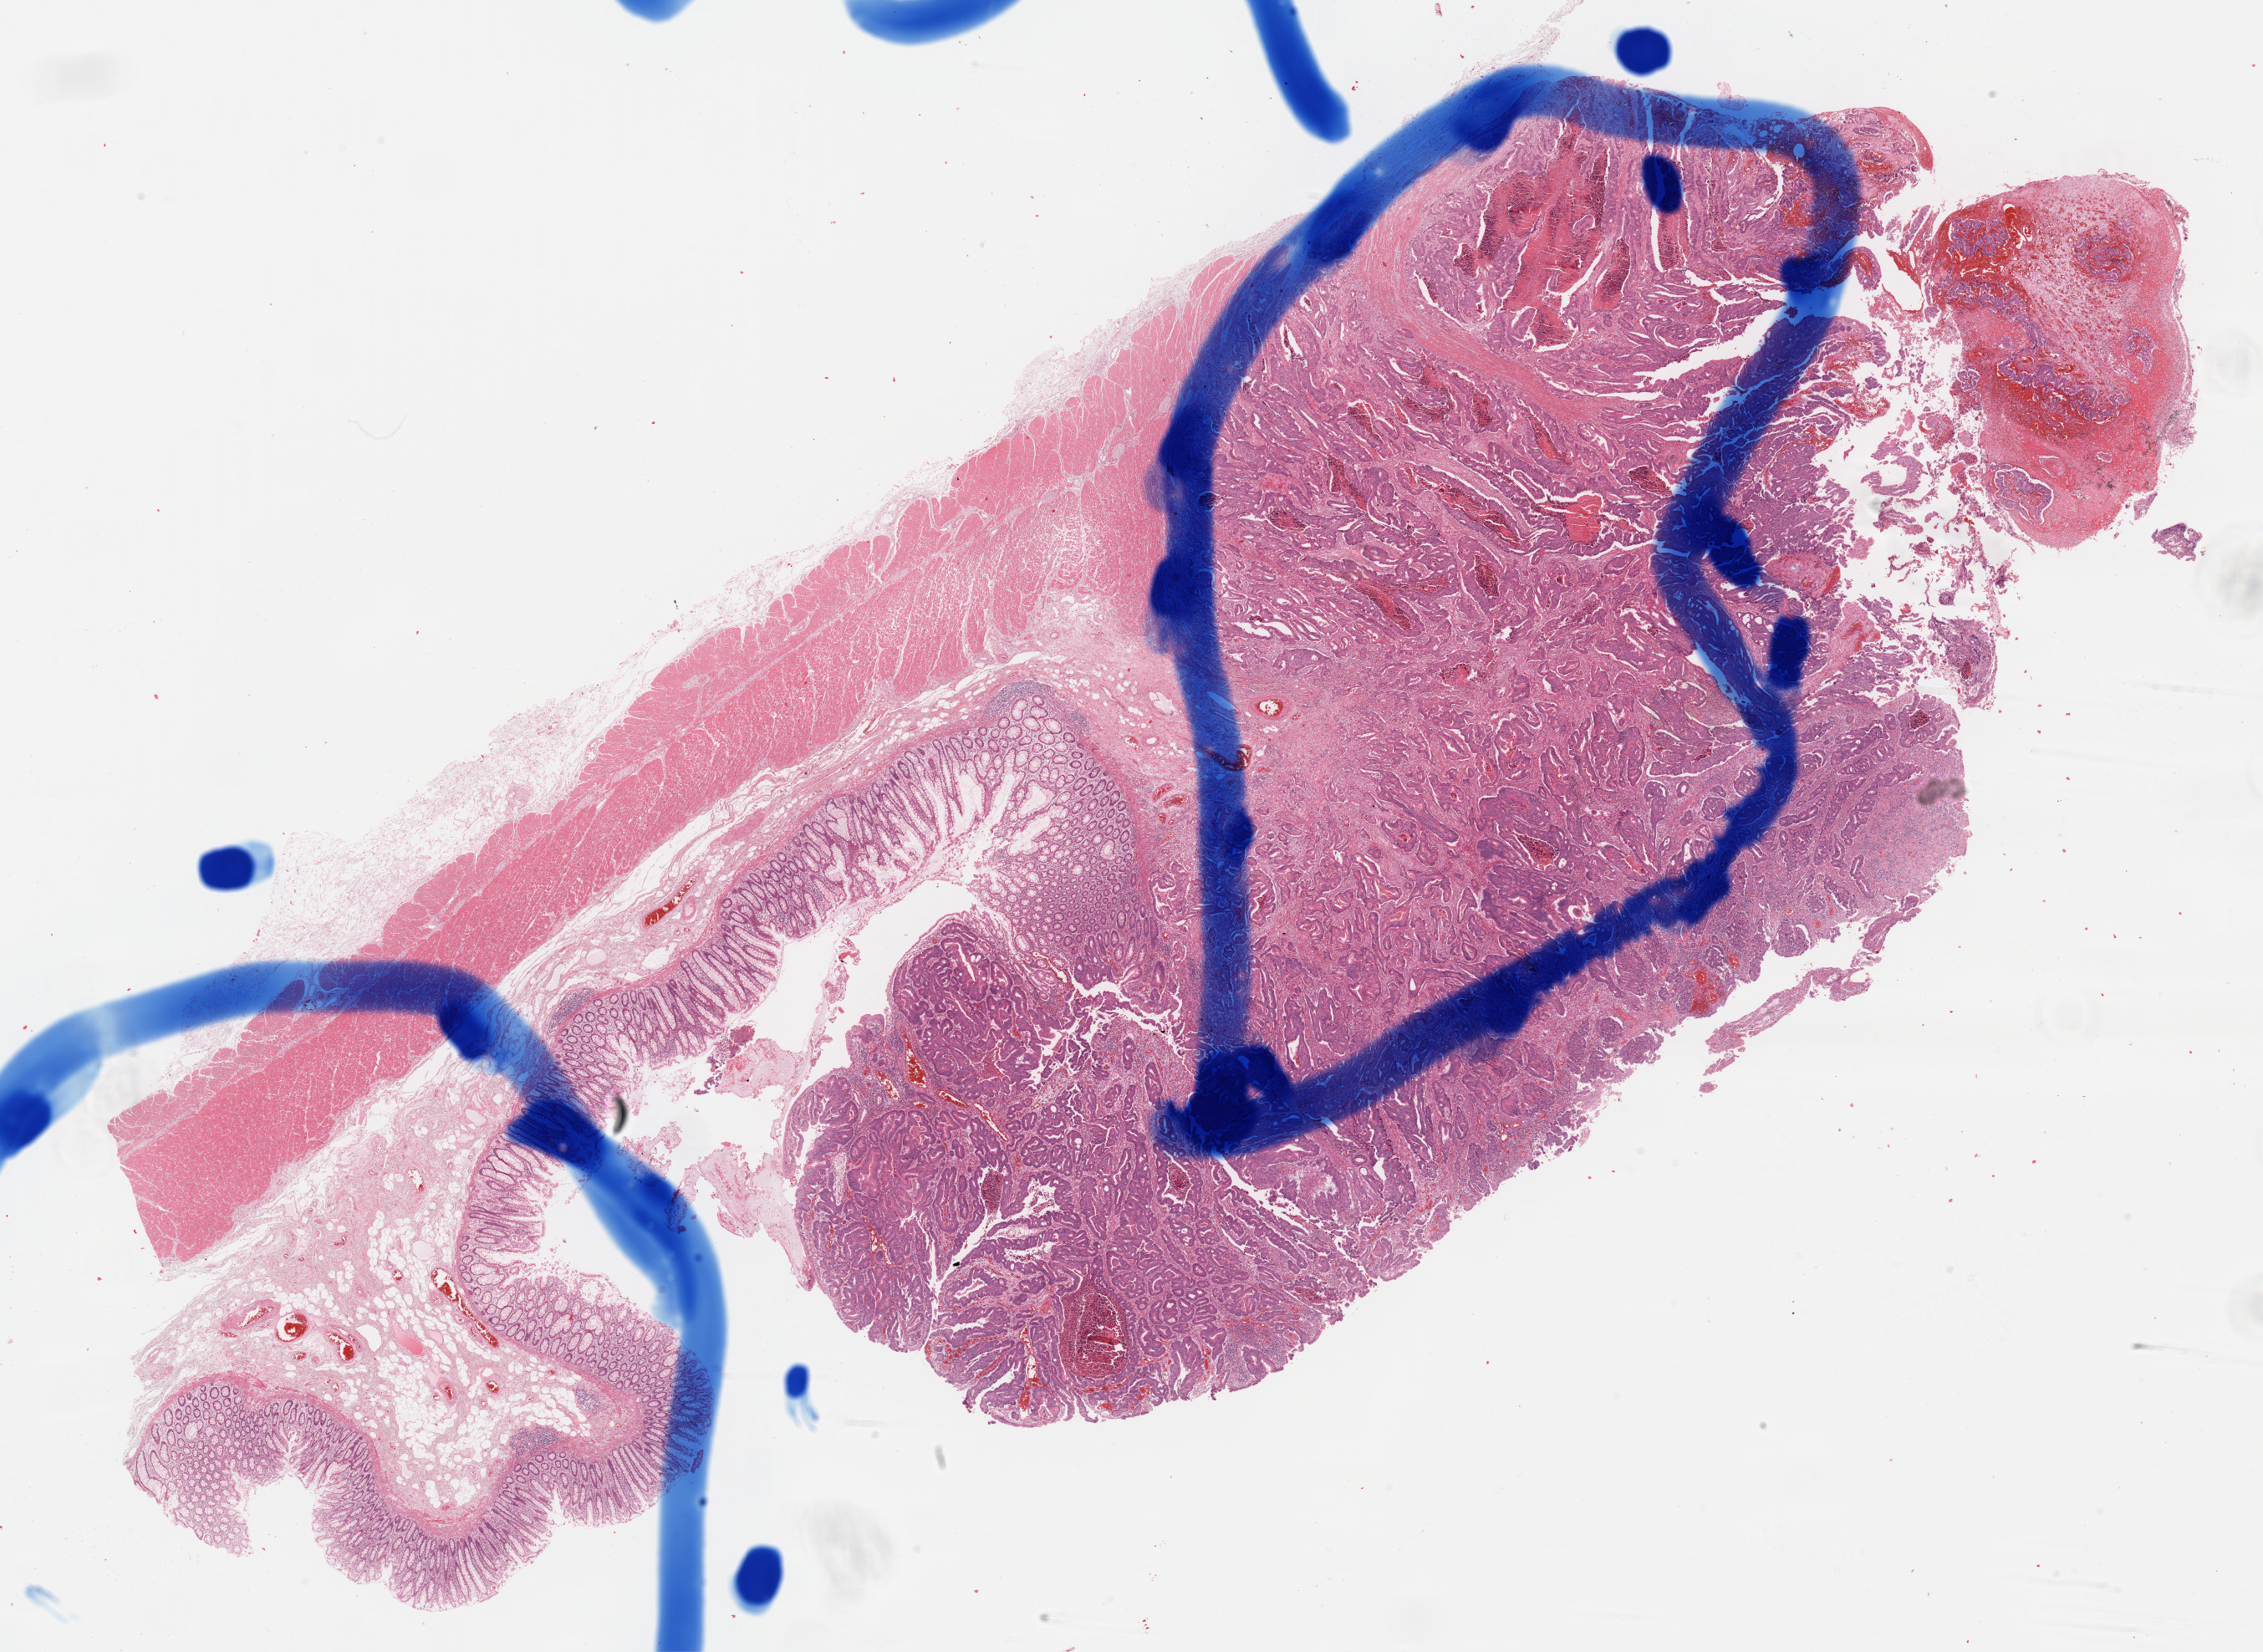
Hematoxylin and eosin (H&E) stained whole-slide image — whole scanned area (about 21.4 x 15.6 mm, acquisition: 40x scan) shown as a low-resolution overview. Formalin-fixed paraffin-embedded (FFPE) diagnostic section. Rectum, primary tumour sample. Patient: female, age at initial diagnosis 73 years.
Diagnosis: Adenocarcinoma, NOS. AJCC pathologic stage: IIIC.